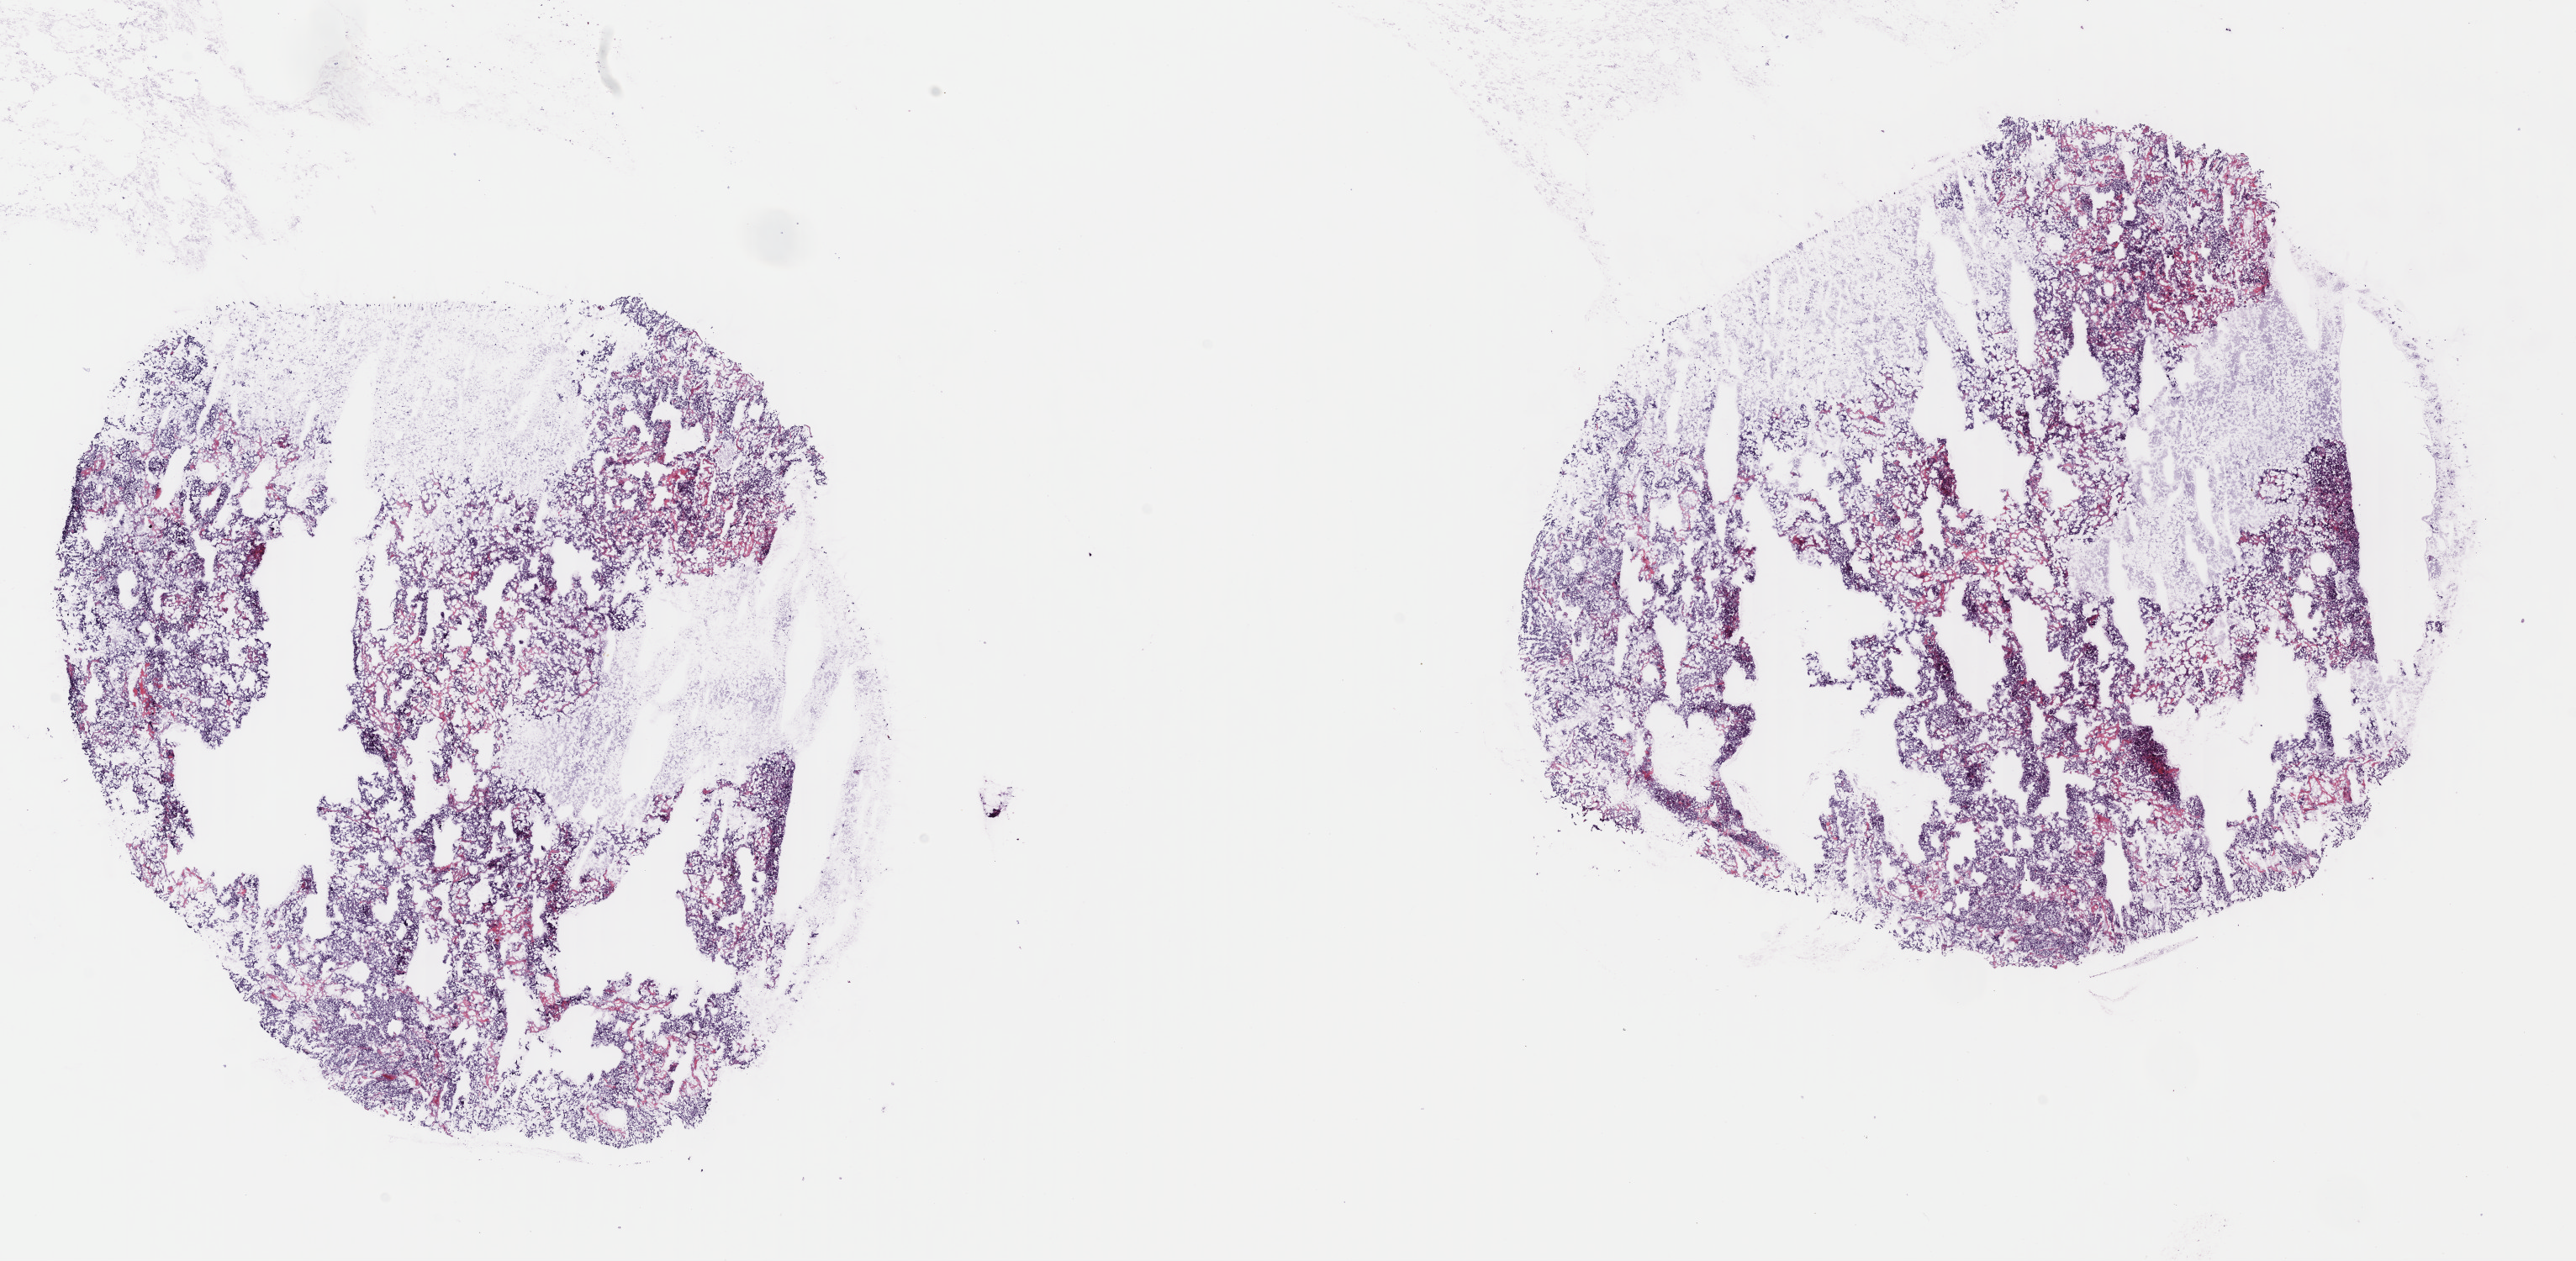
Whole-slide histology image, H&E-stained, a low-resolution overview of the entire scanned area, about 24.1 x 11.8 mm (from a 40x scan); frozen section from the top of the tissue portion; primary tumour sample from the adrenal gland. Male patient; age at initial diagnosis 46 years. Pathologist review of this section (percent, as recorded): tumour cells 80%, tumour nuclei 80%, normal cells 0%, stromal cells 20%, necrosis 0%. Inflammatory infiltration, as recorded: lymphocyte infiltration 0%, monocyte infiltration 0%, neutrophil infiltration 0%.
• pathologic diagnosis: Pheochromocytoma, NOS